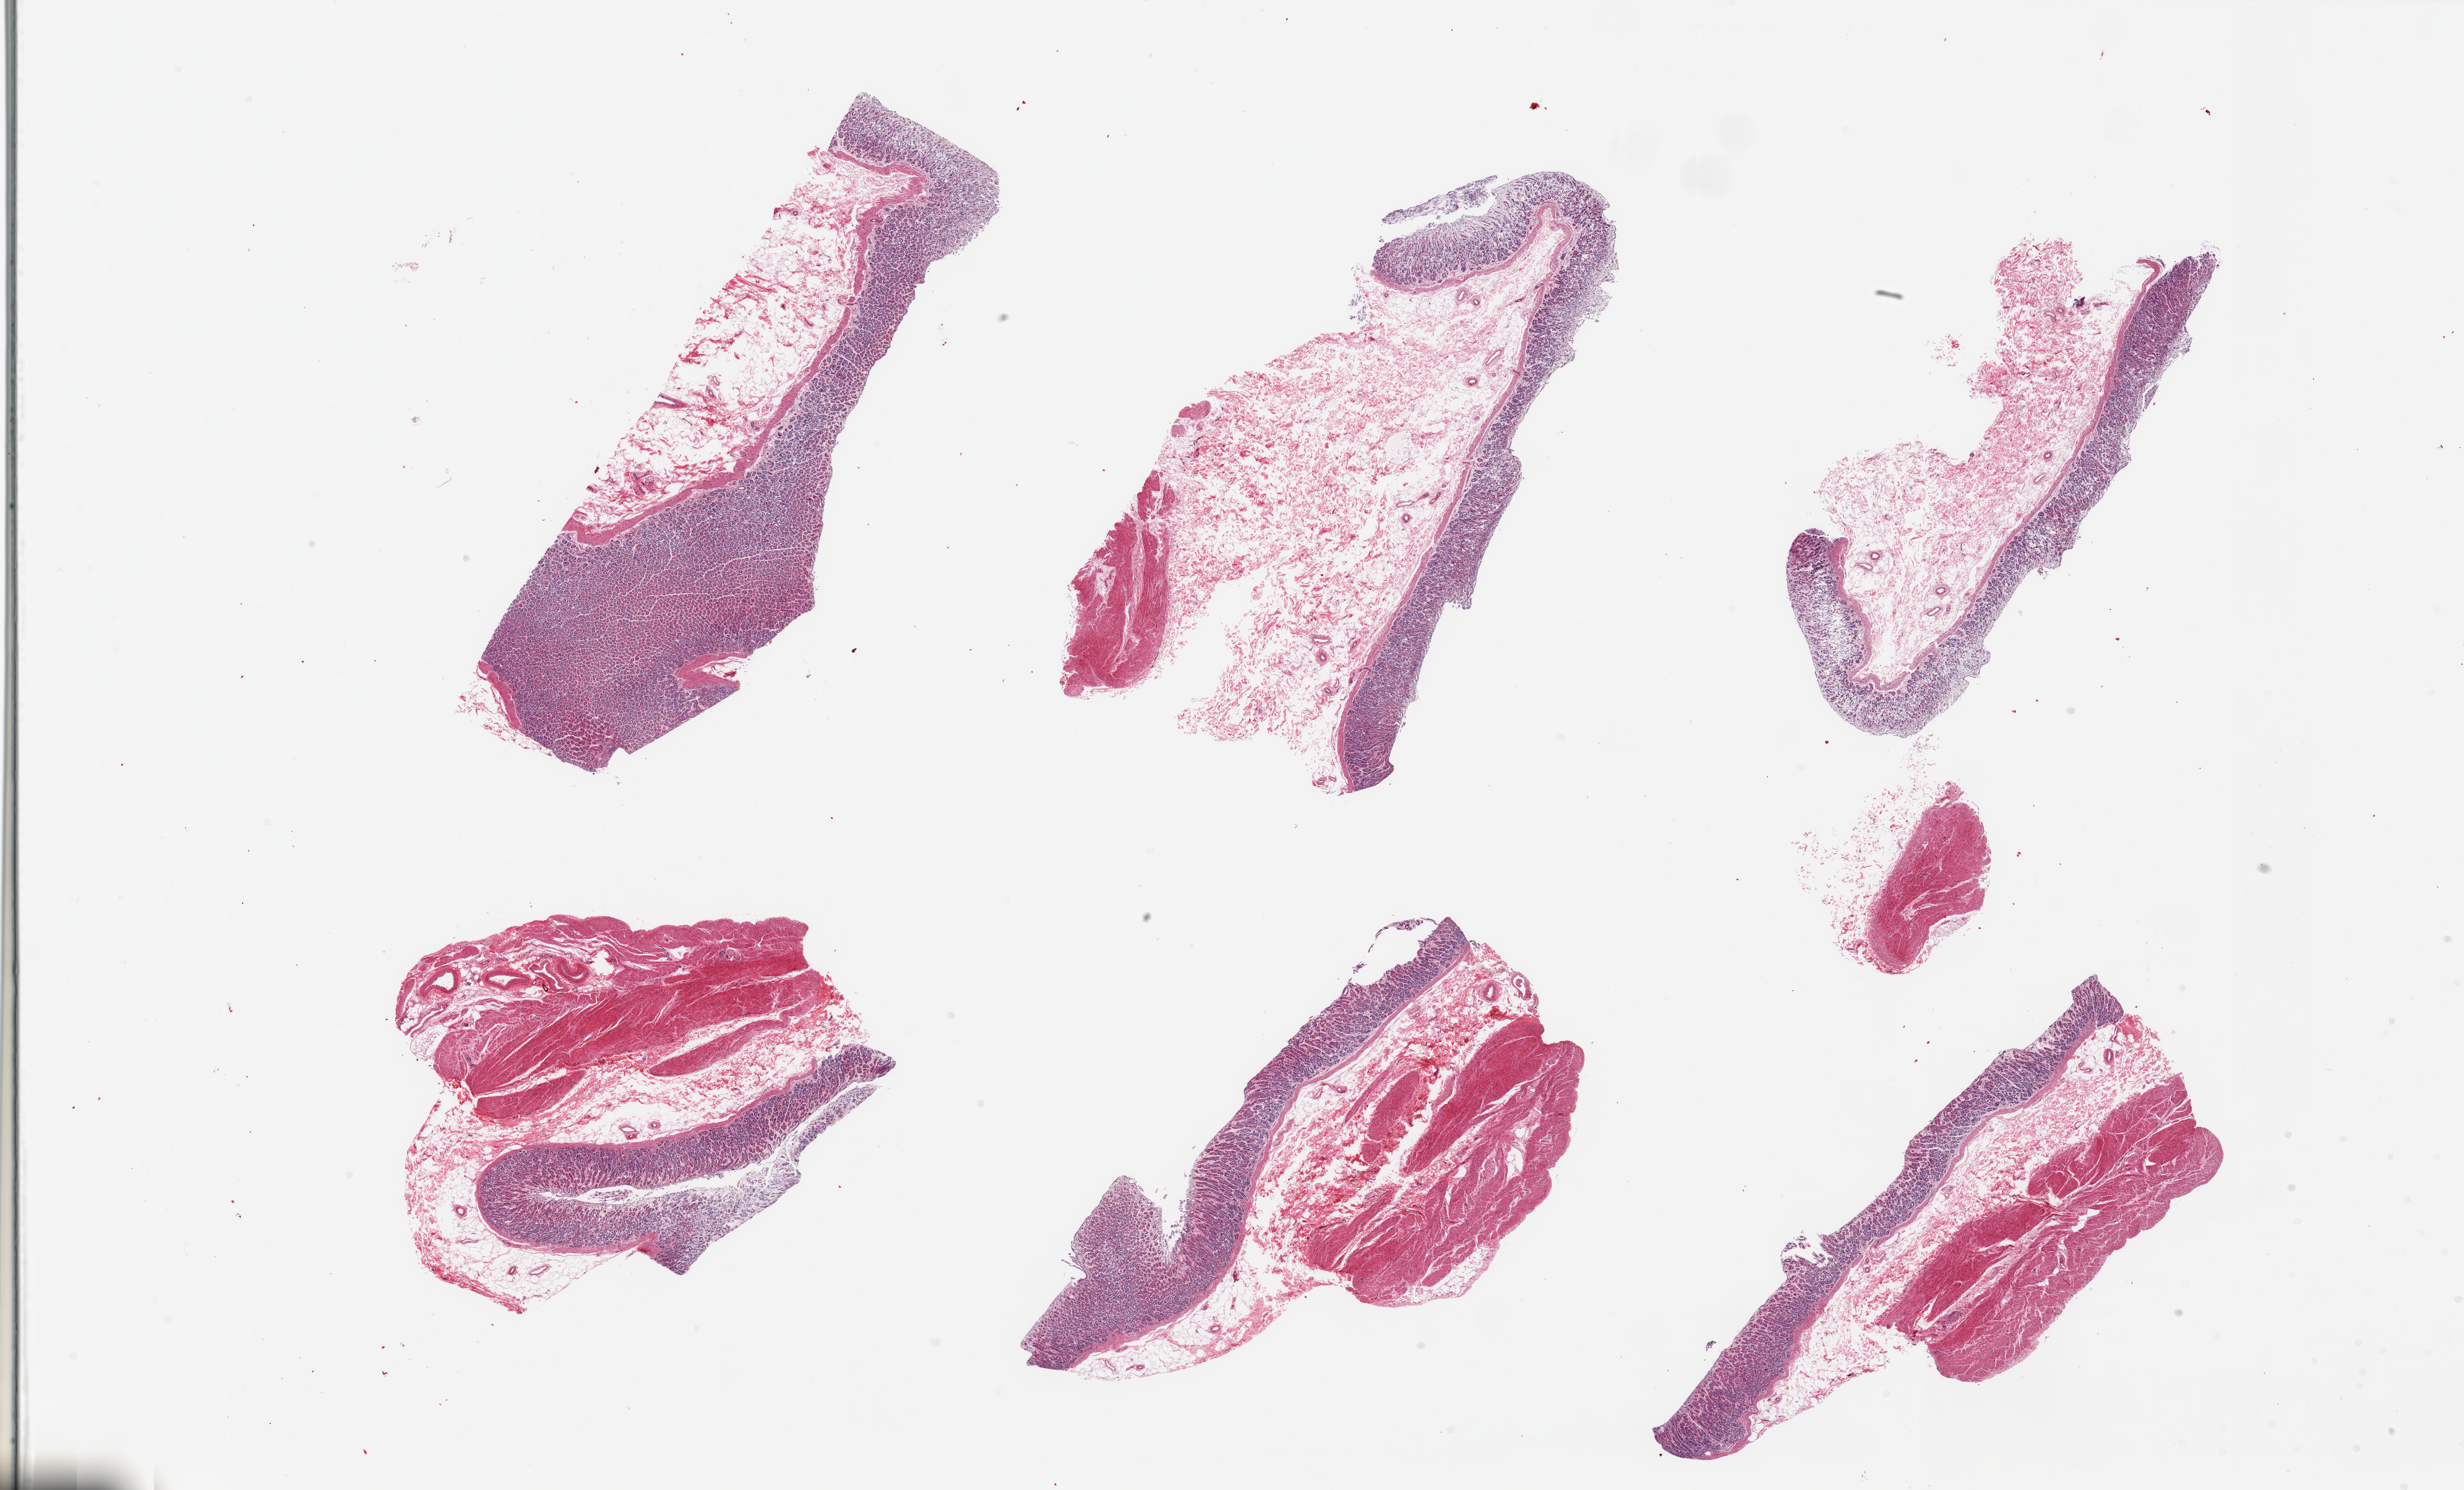
Digitized hematoxylin and eosin (H&E)-stained section, whole scanned area (about 31.5 x 19.1 mm, from a 20x scan) shown as a low-resolution overview, PAXgene-fixed, paraffin-embedded tissue, section of stomach (target tissue), donor tissue sample. Donor sex: male.
Reviewer comment on this tissue sample: 6 pieces, mucosa up to ~0.7mm, moderate-severe autolysis.